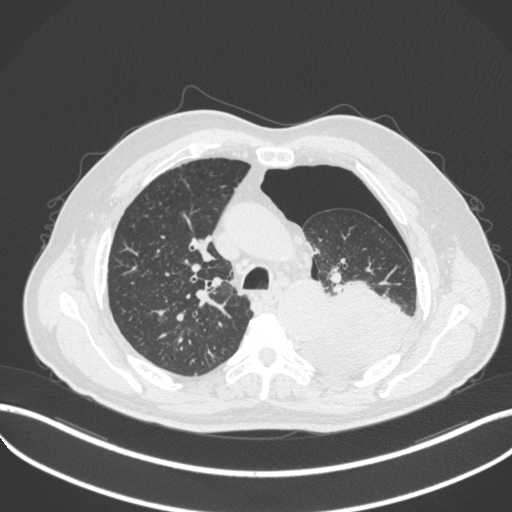
Chest CT, one axial slice. Slice 359 of 466 in the series (ordered by position). Reconstruction kernel B31f. 120 kVp. Lung window (W 1500 / L -600 HU). 1 mm slice thickness. 512 × 512 image matrix, field of view 400 × 400 mm. Male patient, age 76 years. From the clinical record (not read from this slice): clinical TNM (as recorded): T3 N0 M1b.
Outlined on this slice (bounding box drawn by a radiologist):
- lung tumour (recorded histology: adenocarcinoma): bounding box [x1, y1, x2, y2] px = [304, 278, 414, 375]